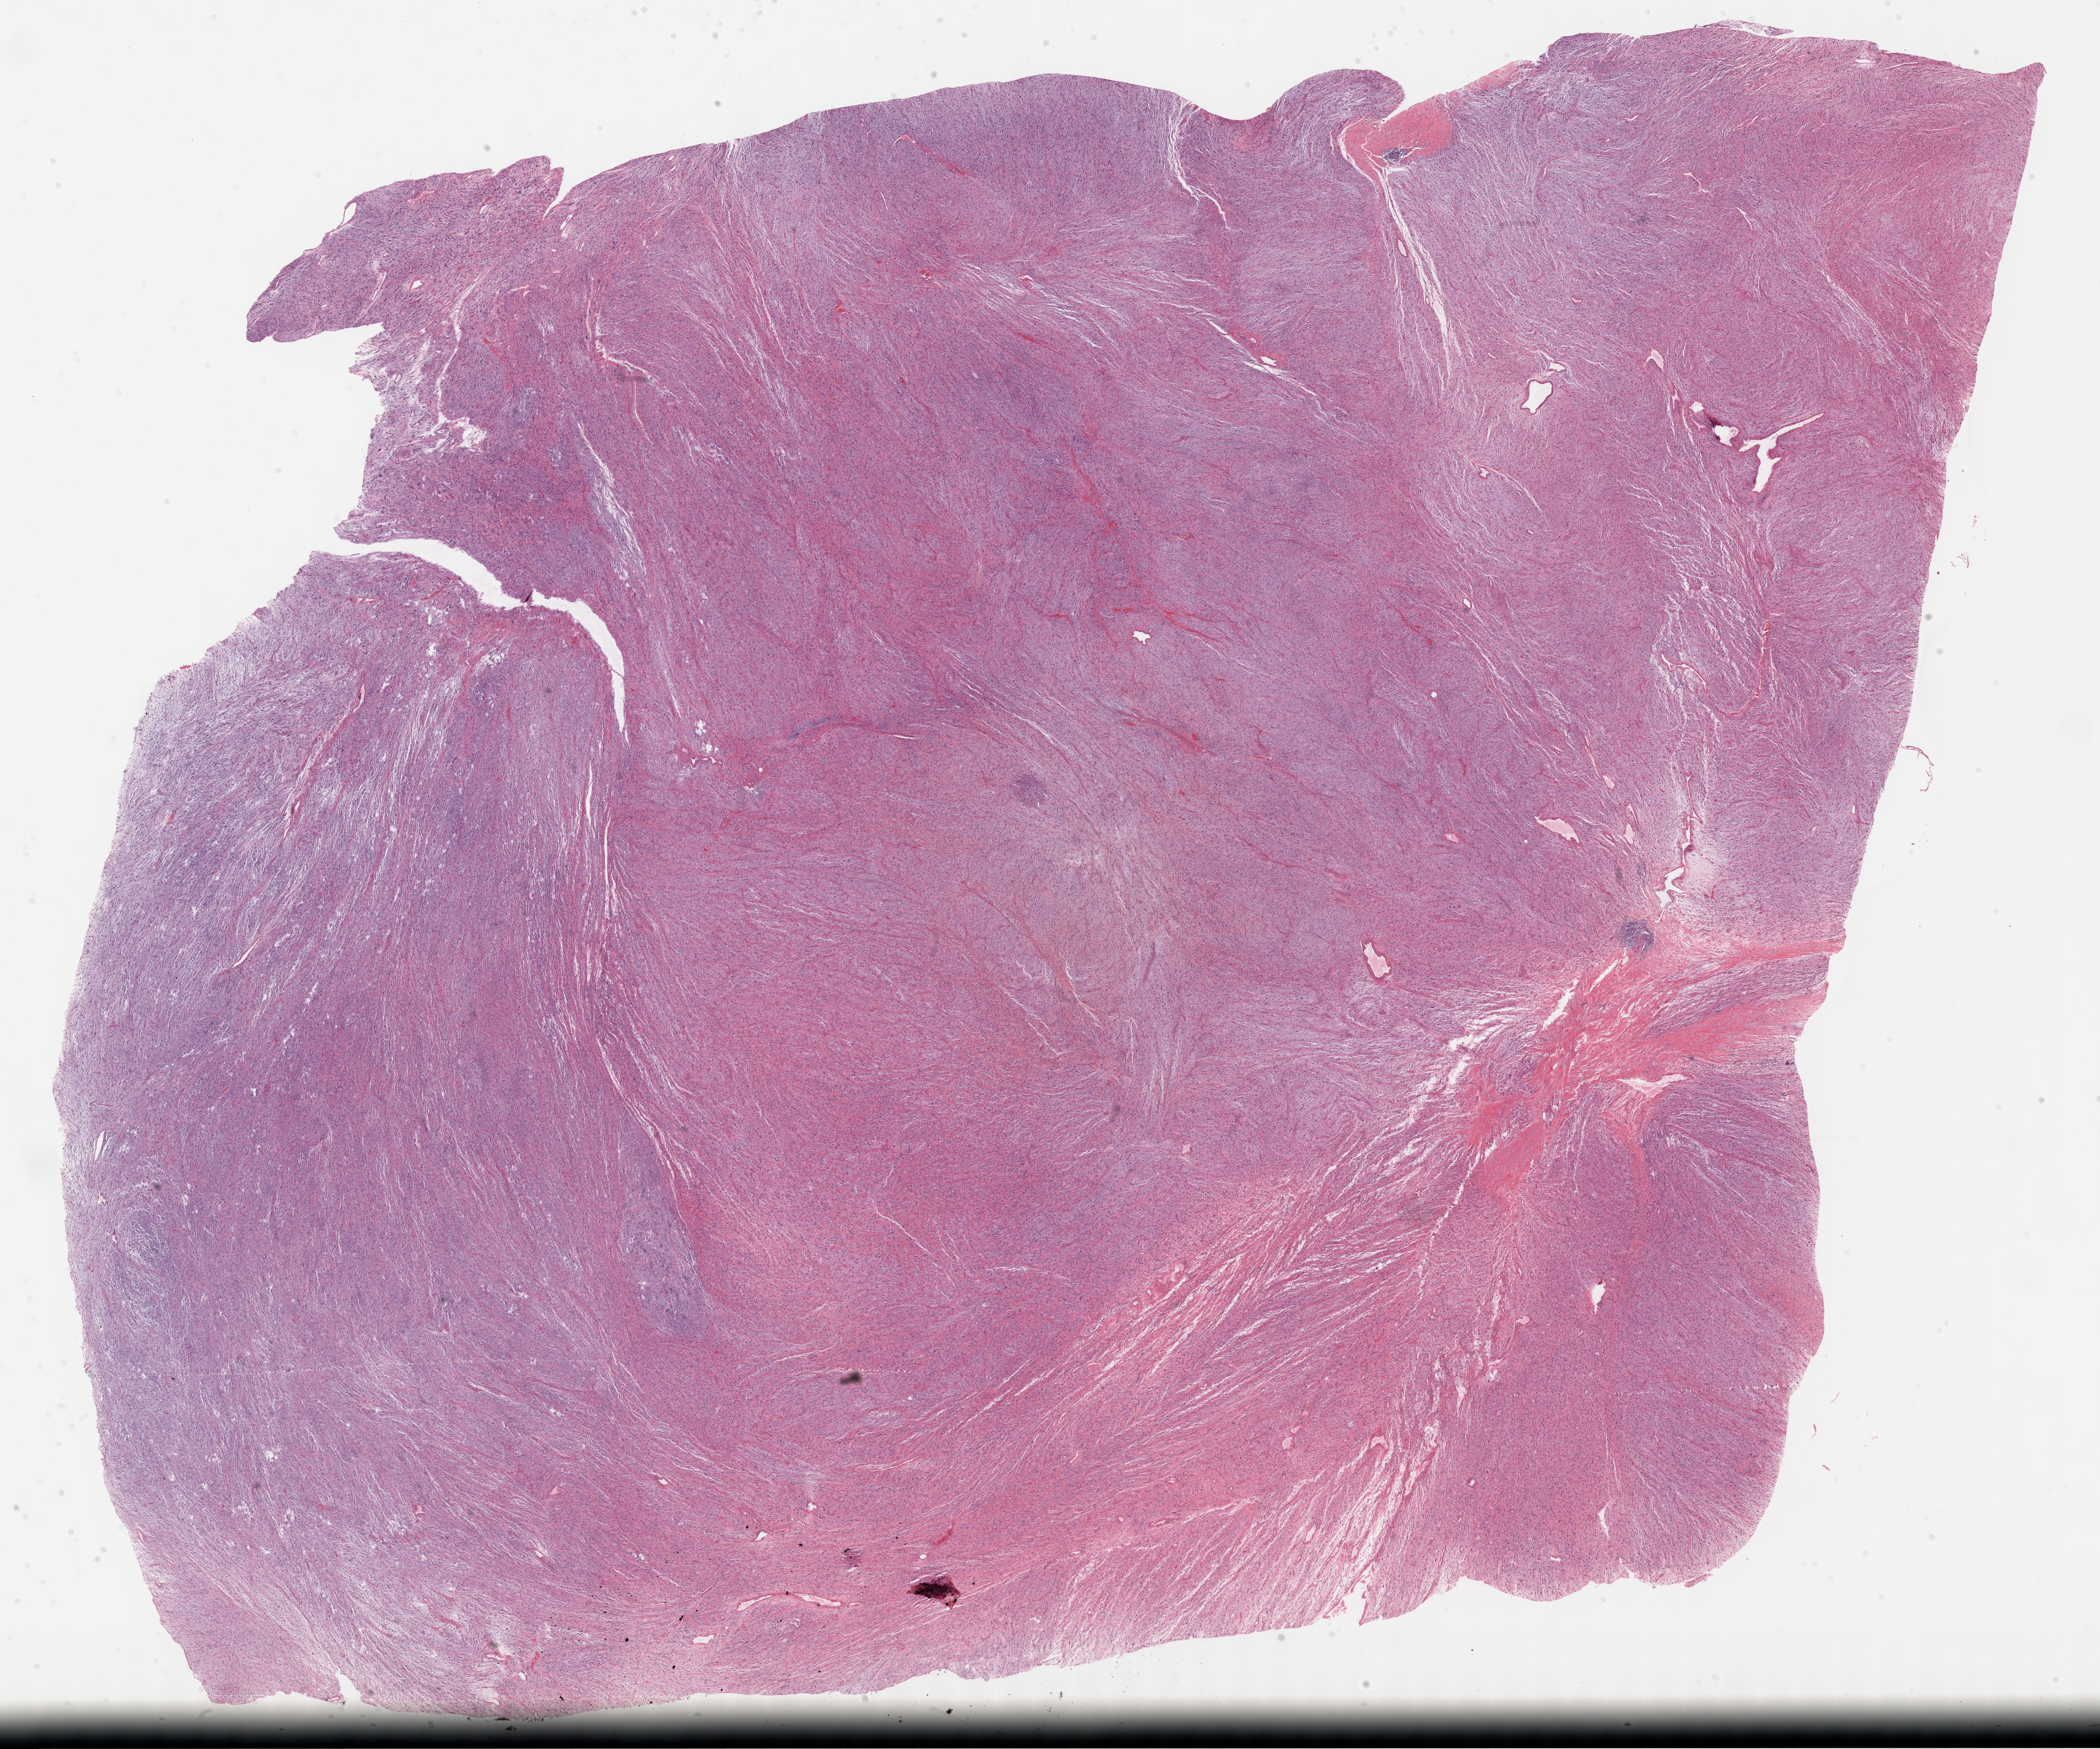
Digitized Hematoxylin and eosin (H&E) stained tissue section (whole slide) — shown as a low-resolution overview of the whole scanned area (about 27.7 x 23.1 mm). Formalin-fixed paraffin-embedded (FFPE) diagnostic section. Connective, subcutaneous and other soft tissues, primary tumour sample. Patient: male, age at initial diagnosis 59 years.
Pathologic diagnosis: Fibromyxosarcoma.